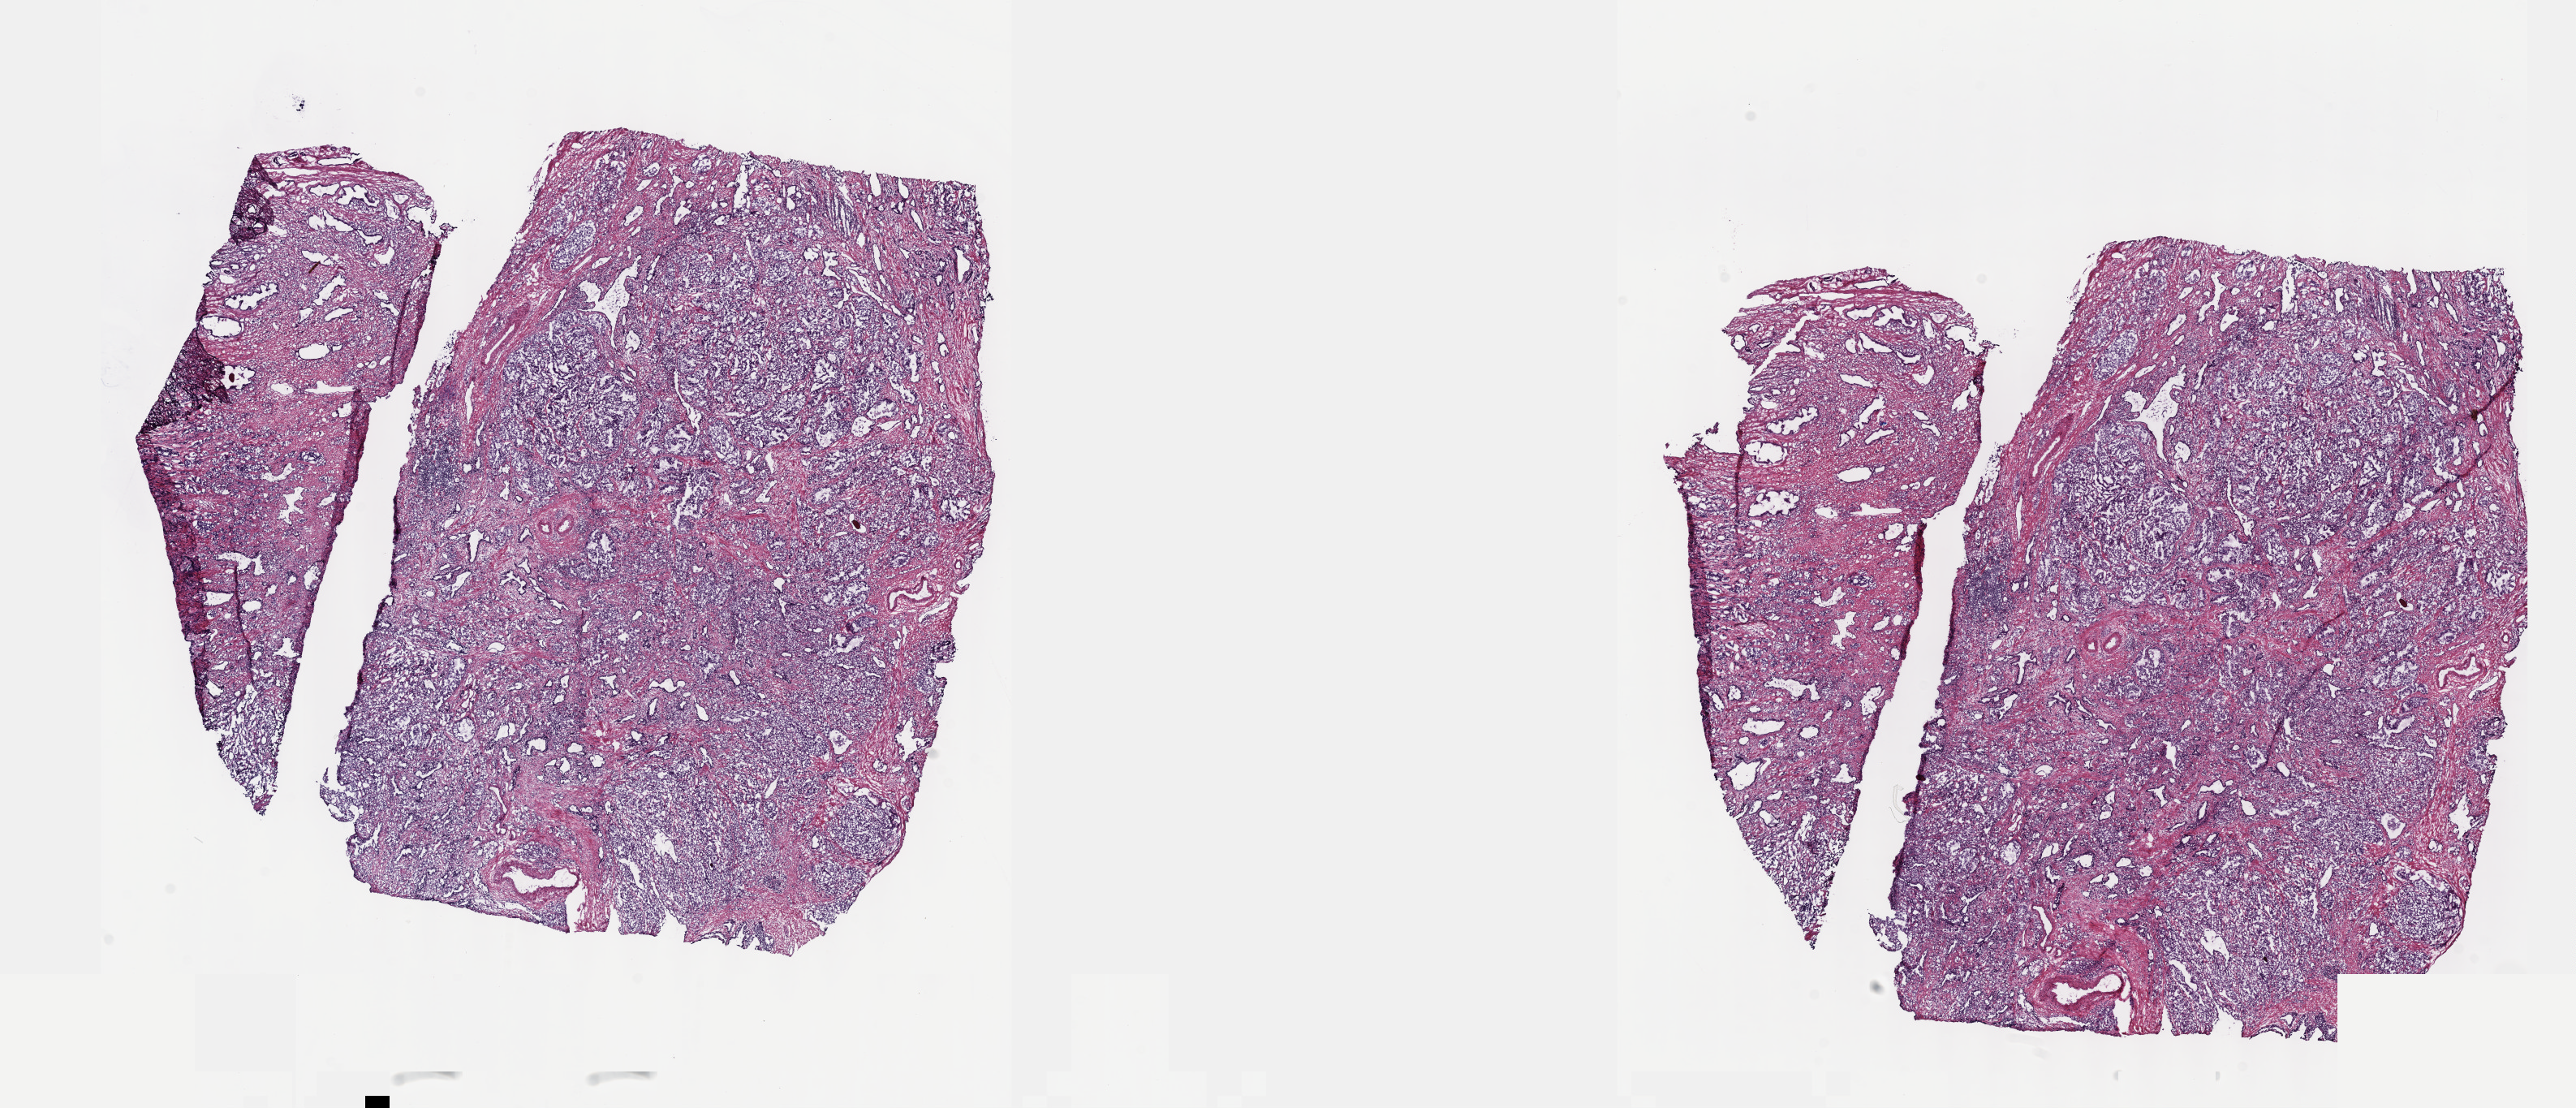
H&E-stained whole-slide image, a low-resolution overview of the entire scanned area, about 25.7 x 11.0 mm (slide scanned at 40x); frozen section; sample: primary tumour, prostate. Patient: male, age at initial diagnosis 52 years. Gleason score: 9 (4+5). Slide review estimates, as recorded: tumour cells 100%, tumour nuclei 85%, normal cells 0%, stromal cells 0%, necrosis 0%. Inflammatory infiltration, as recorded: lymphocyte infiltration 0%, monocyte infiltration 0%, neutrophil infiltration 0%.
* lymph nodes positive (case pathology): 1 of 10 examined
* laterality: bilateral
* pathologic diagnosis: Adenocarcinoma, NOS (prostate gland)